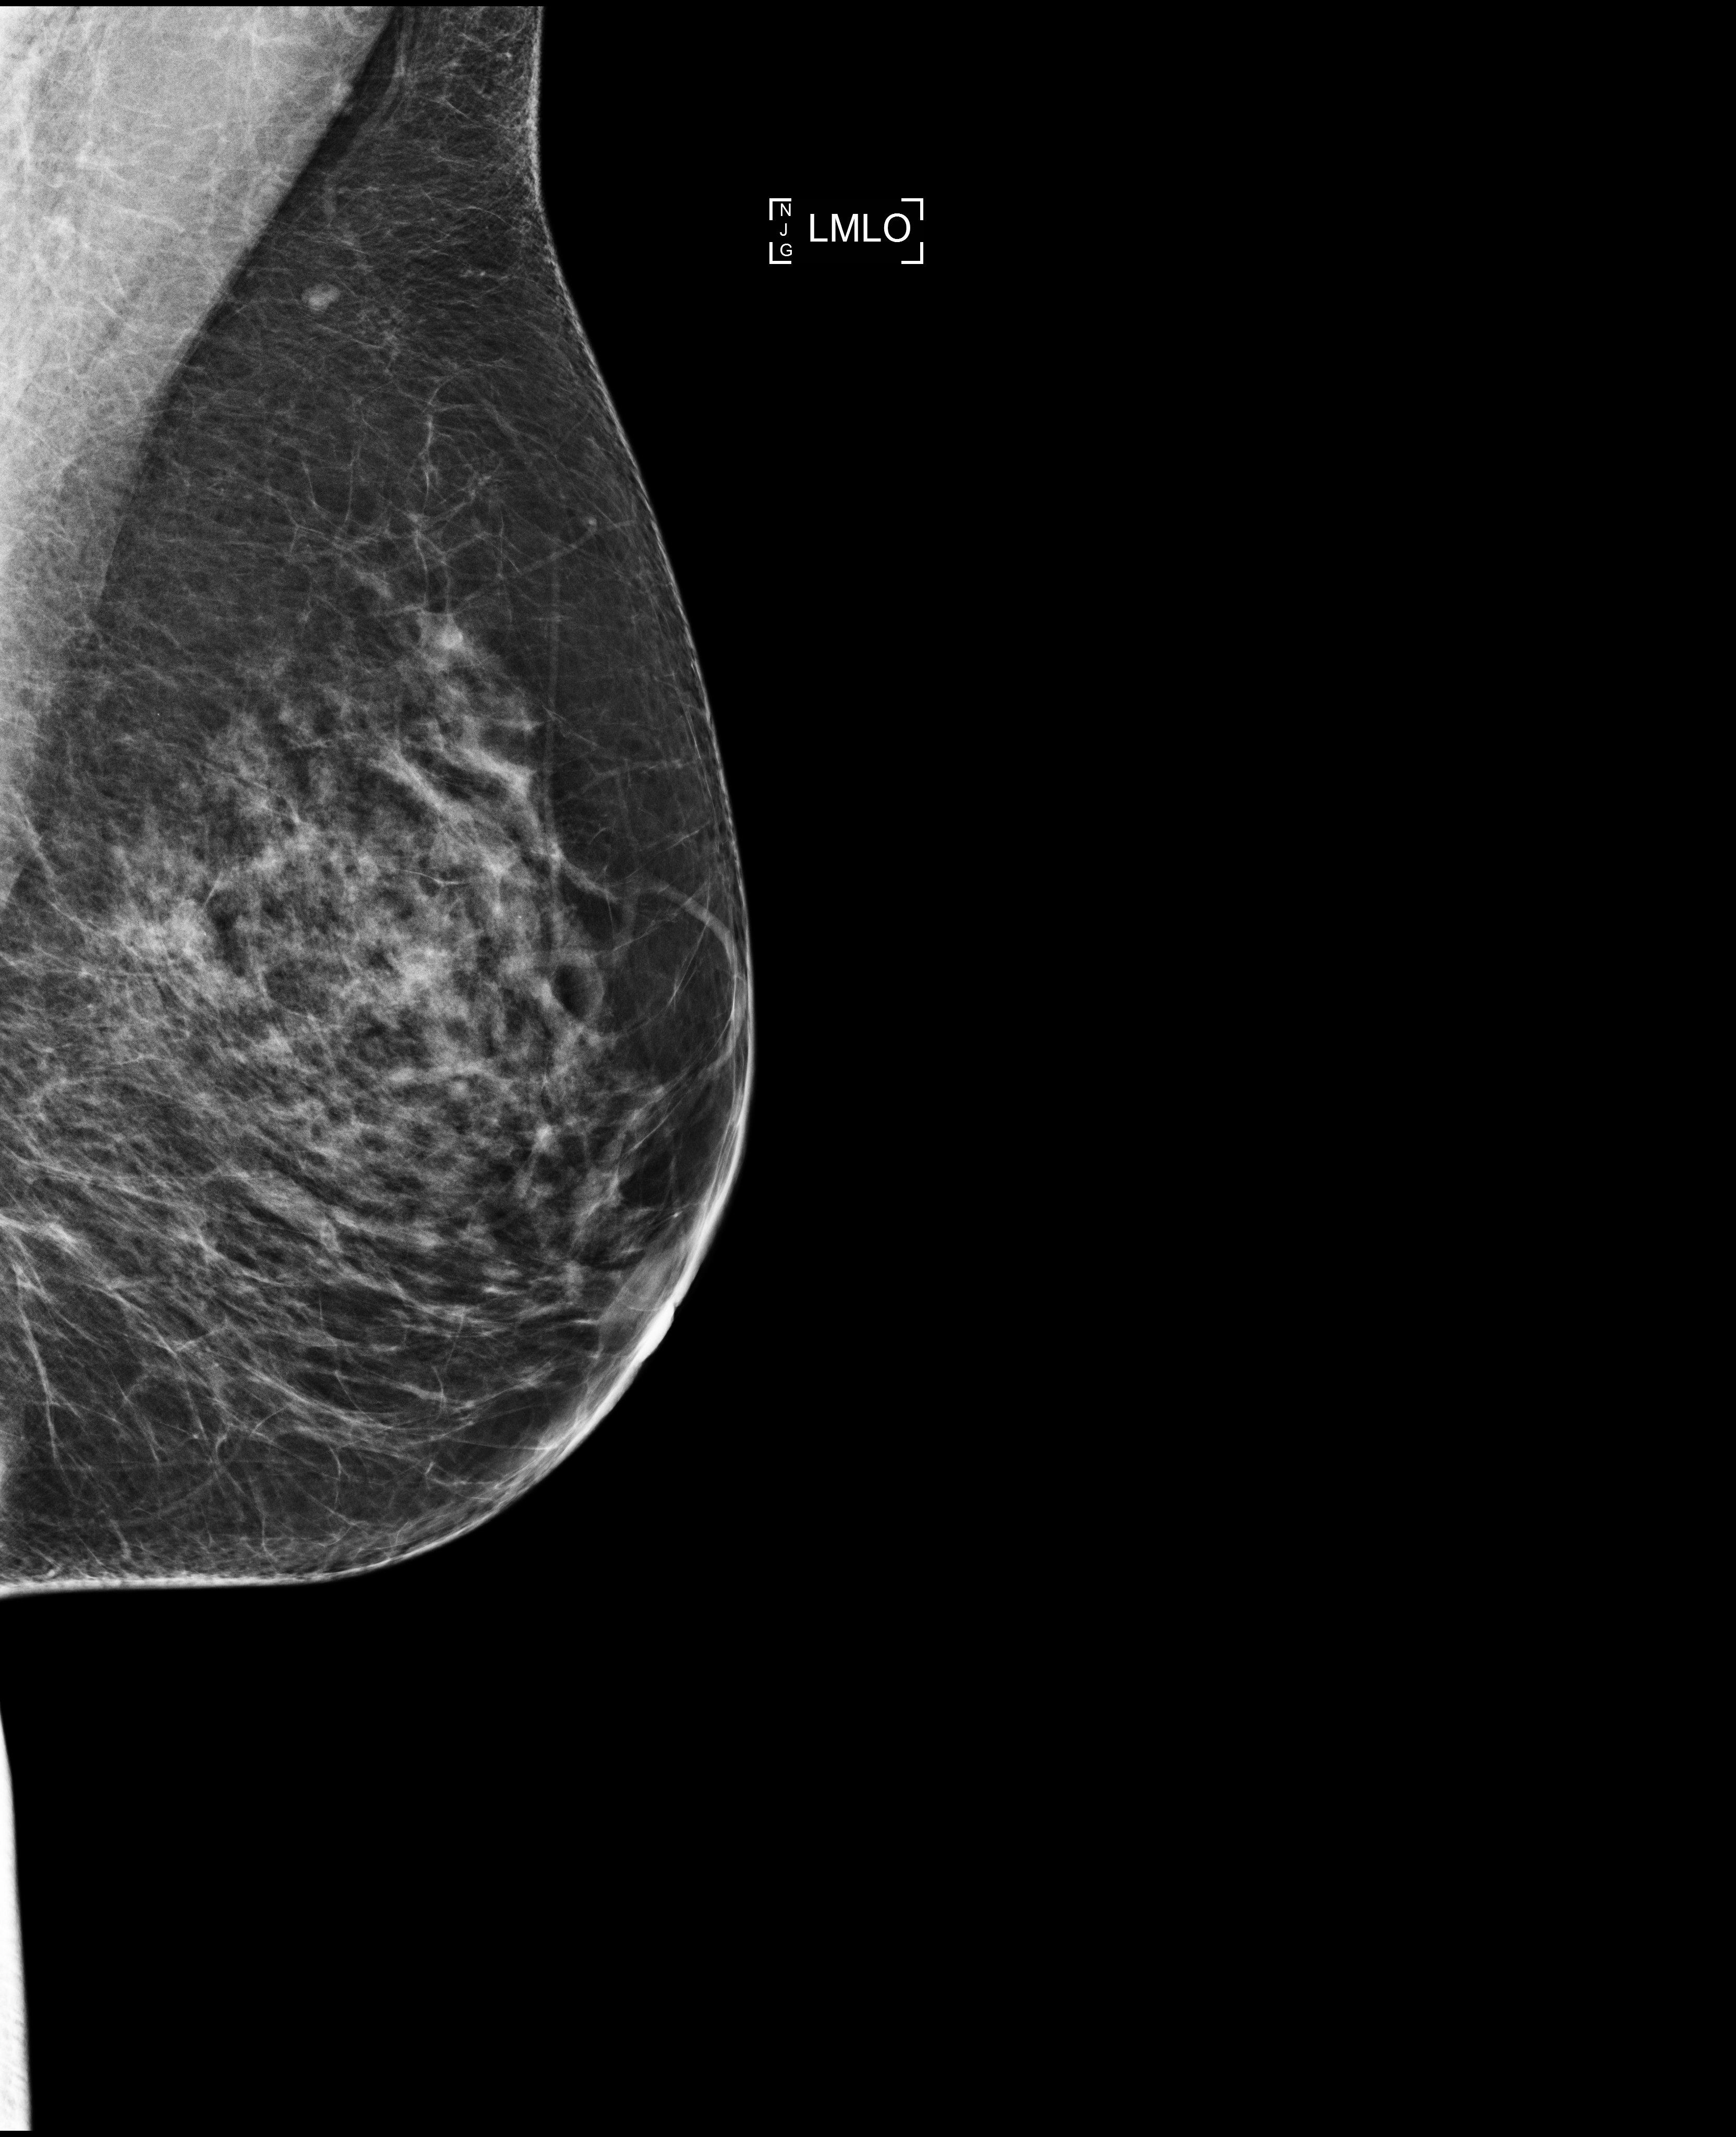
Annual screening mammography examination; compressed breast thickness 75 mm; system: Selenia Dimensions. Female patient, age 53 years.
Image type: full-field digital mammogram. Breast: left. Projection: MLO view.